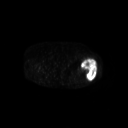
FDG PET of an extremity soft-tissue mass (from a PET/CT study), one axial slice; slice 241 of 267 in the series (ordered by position); 128 × 128 image matrix, field of view 700 × 700 mm. Patient: female, 62 years. Case-level facts recorded for this patient, not image findings: histological type: undifferentiated – high grade; grade: high; site of the primary tumour: left thigh.
Structures marked on this image (expert contour drawn on MRI and transferred to this co-registered scan by the dataset authors):
- gross tumour volume including surrounding oedema: bounding box <81,58,97,81> (left, top, right, bottom; pixels)
- gross tumour volume (mass): <81,58,97,81>